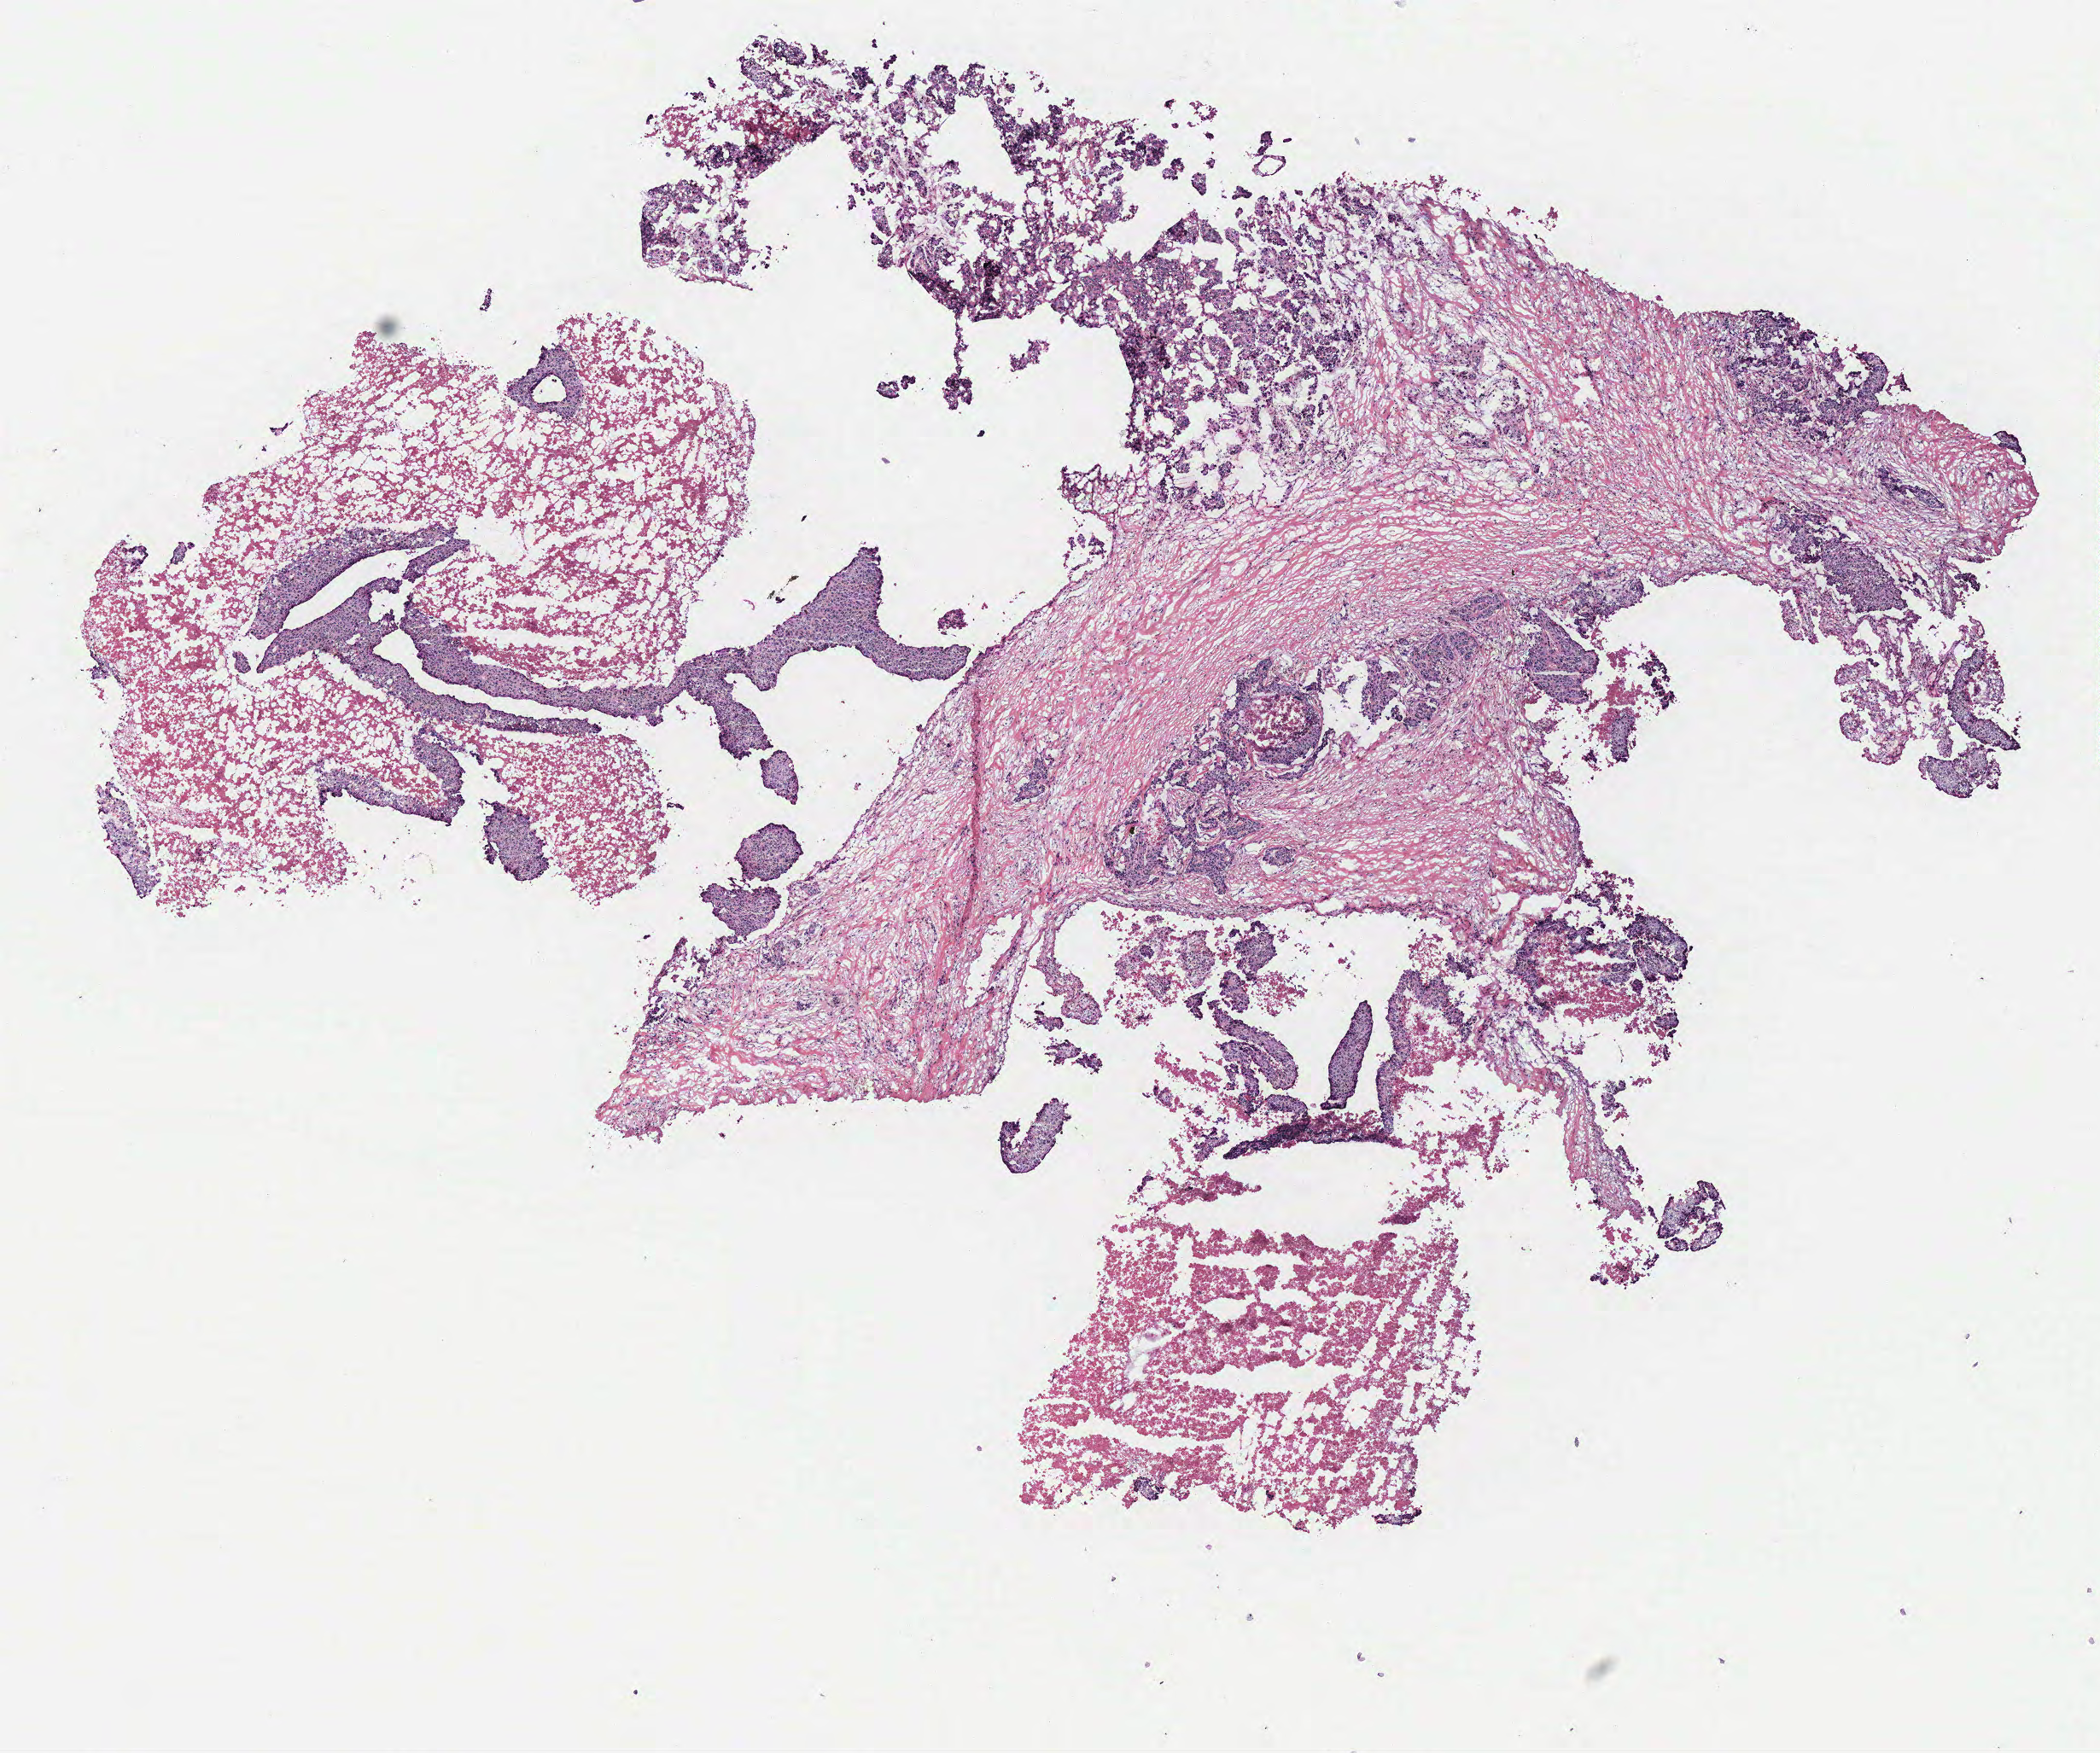
Whole-slide histology image, H&E, whole scanned area (about 9.8 x 8.2 mm) shown as a low-resolution overview, breast, tissue type not recorded.
Patient diagnosis (cohort enrolment): breast cancer (breast).